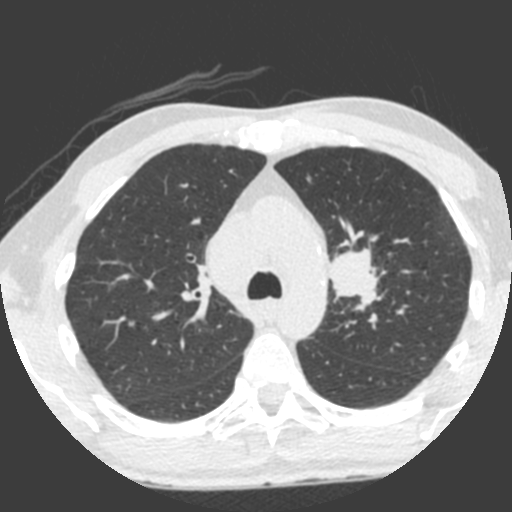
Low-dose screening chest CT, one axial slice; slice 152 of 212 in the series (ordered by position); 120 kVp; lung window (W 1500 / L -600 HU); 2 mm slice thickness; 512 × 512 image matrix, field of view 315 × 315 mm.
Outlined on this slice (expert manual segmentation):
- lesion 1 (tumor, upper lobe of left lung): box from (x=329, y=247) to (x=379, y=311) px